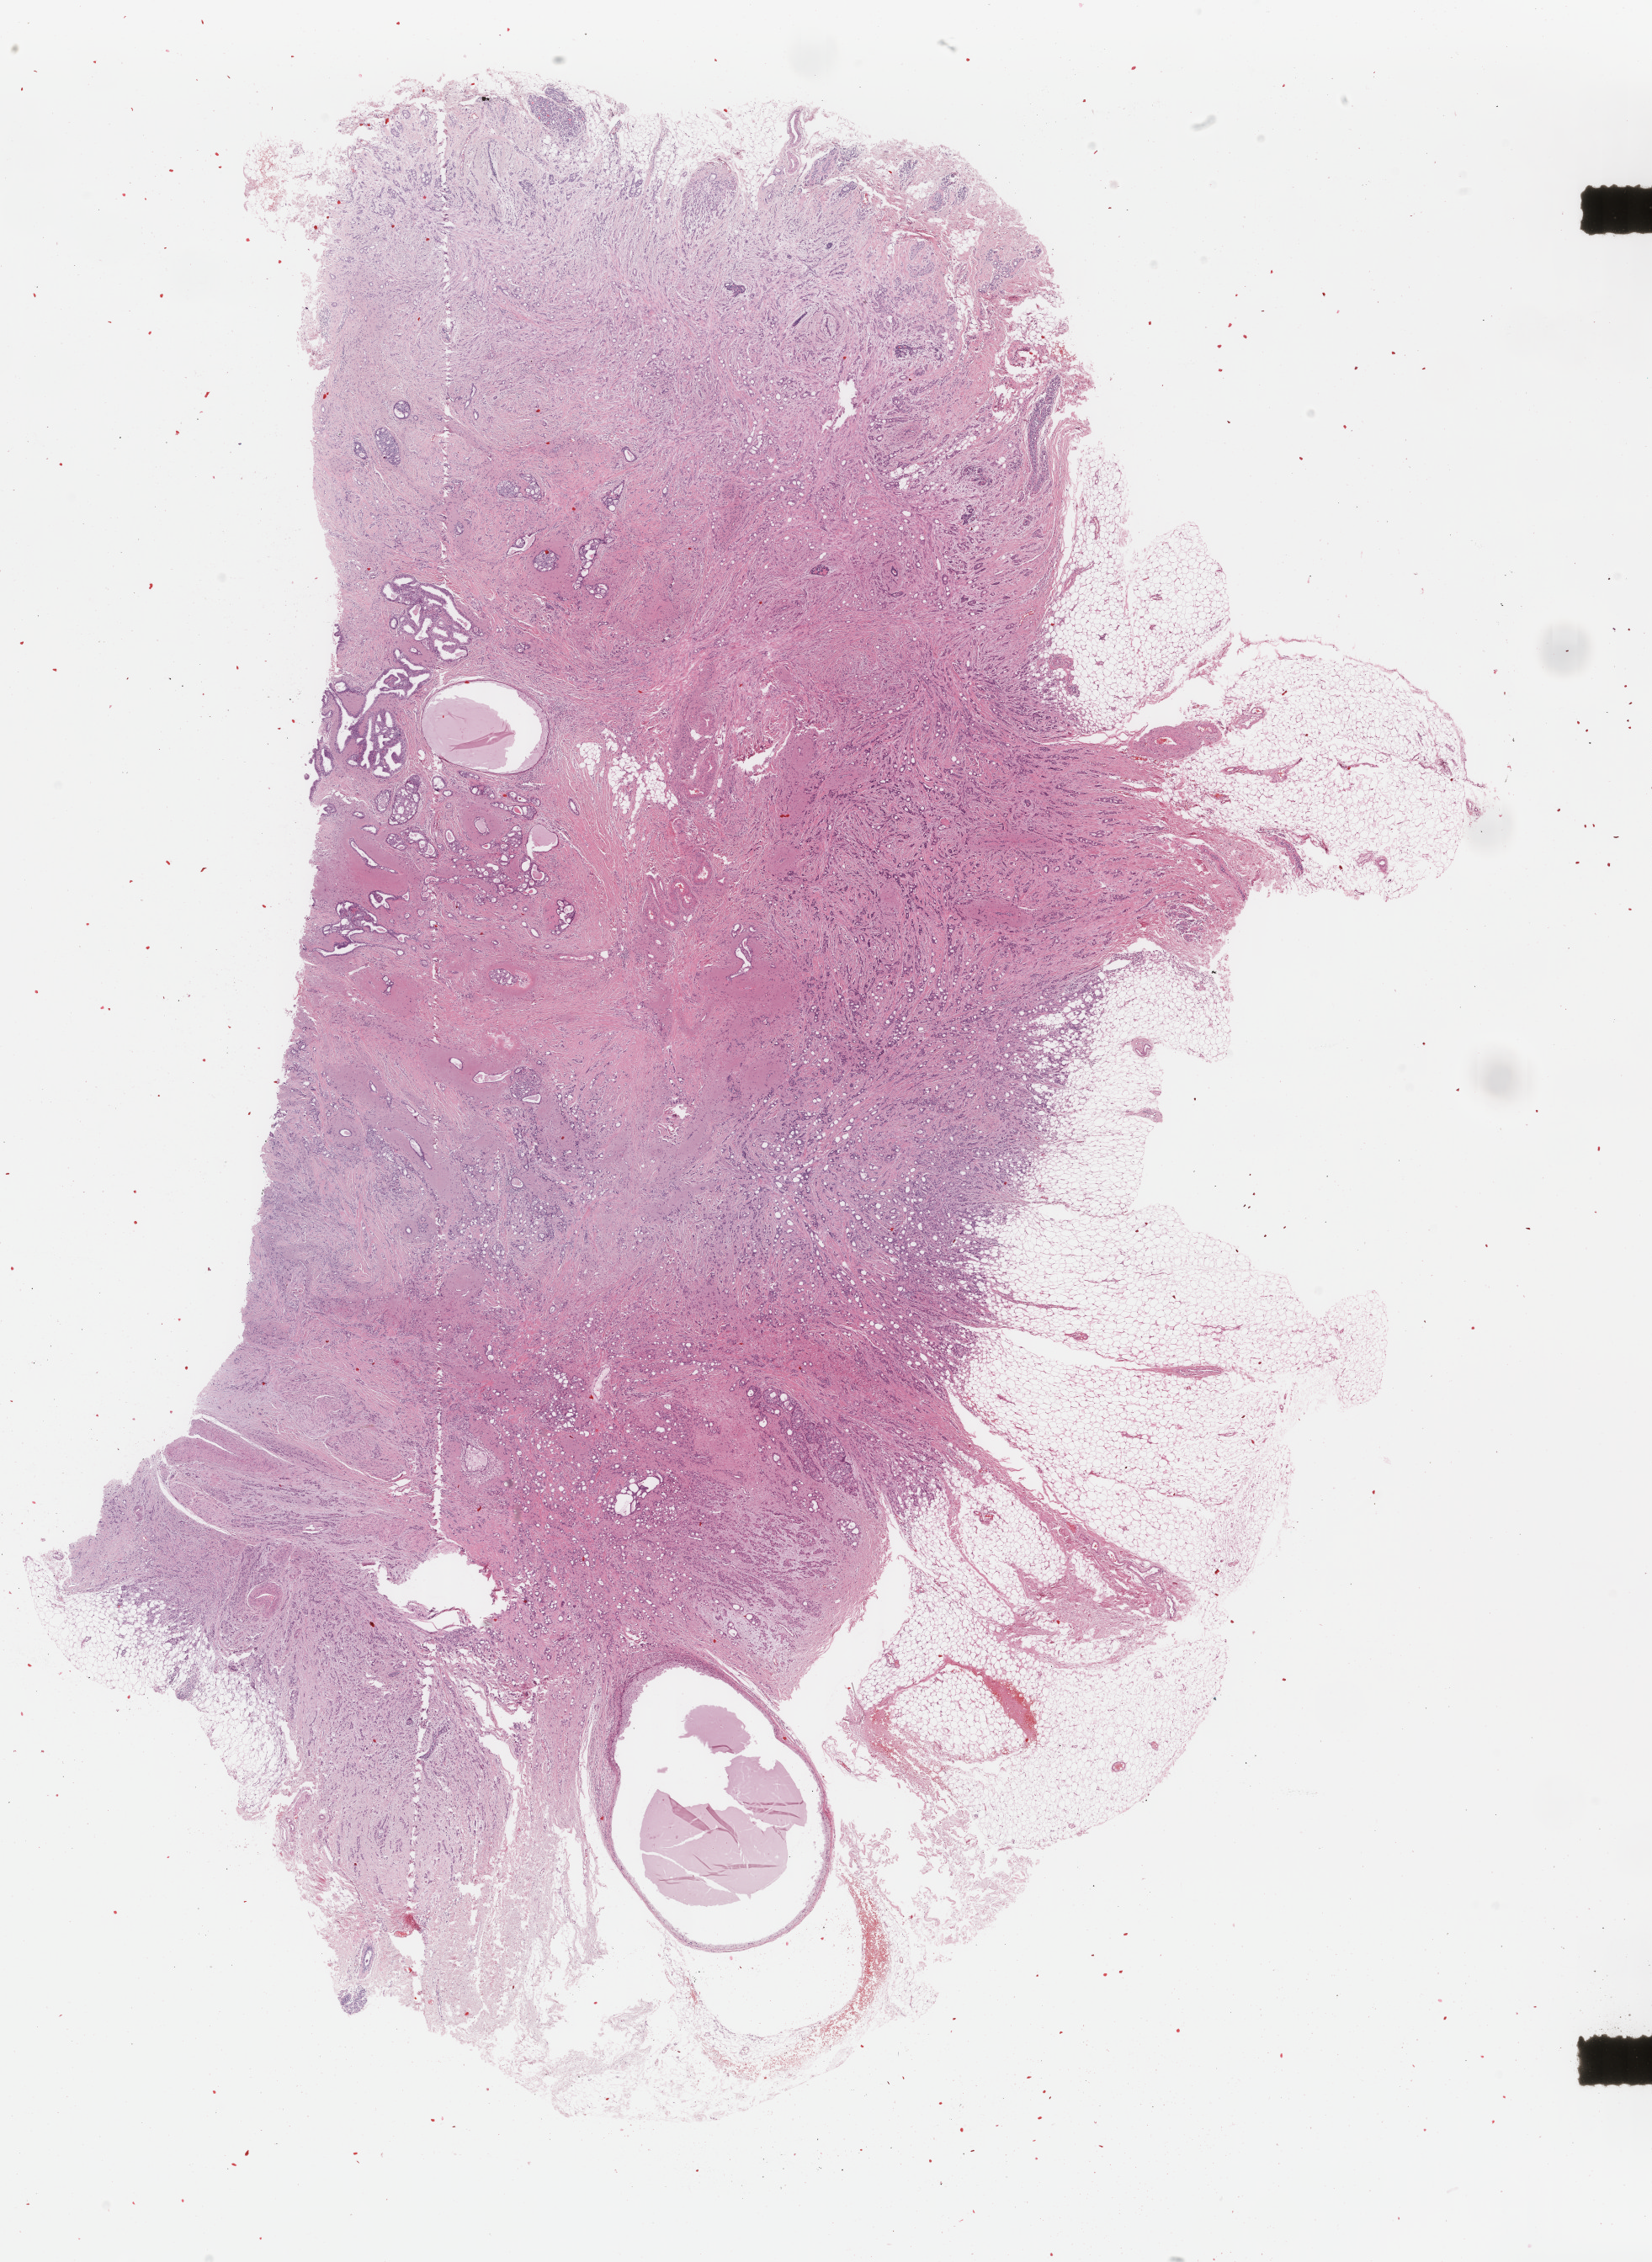
Digitized H&E tissue section (whole slide) — a low-resolution overview of the entire scanned area, about 15.6 x 21.3 mm (acquisition: 40x scan); formalin-fixed paraffin-embedded (FFPE) diagnostic section; sample: primary tumour, breast. Female, age 51 years at initial diagnosis.
• diagnosis: Infiltrating duct carcinoma, NOS
• lymph nodes positive (case pathology): 0 of 1 examined
• AJCC pathologic stage: IA (7th edition)